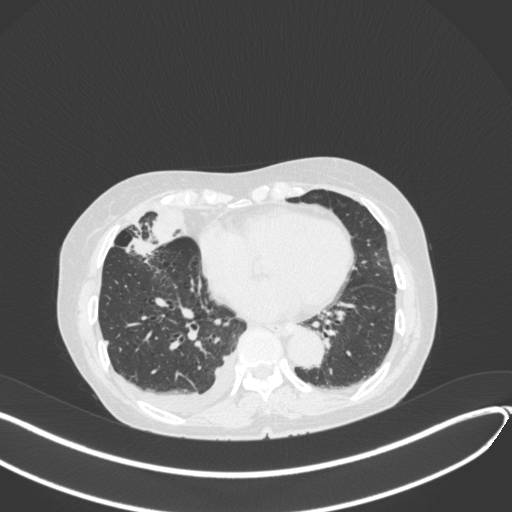
Chest CT, one axial slice. Slice 143 of 418 in the series (ordered by position). Lung window (W 1500 / L -600 HU). 1 mm slice thickness. 512 × 512 image matrix, field of view 400 × 400 mm. Patient: female, 75 years. Case-level facts recorded for this patient, not image findings: clinical TNM (as recorded): T2a N3 M0.
Structures marked on this image (rectangle marked by the reading radiologist):
- lung tumour (recorded histology: adenocarcinoma): bounding box <120,236,160,260> (left, top, right, bottom; pixels)